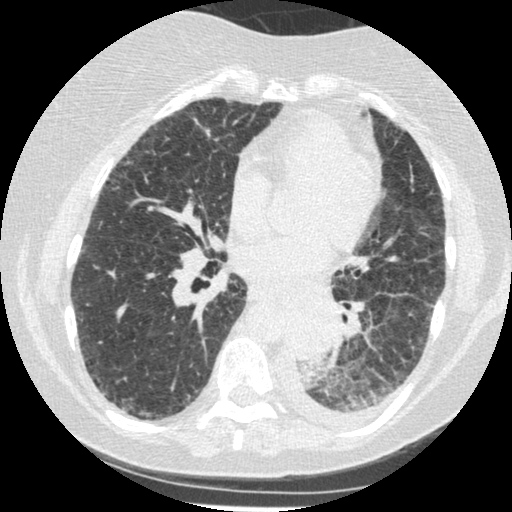
Low-dose screening chest CT, axial slice. Third screening round (two years after baseline). Lung window (W 1500 / L -600 HU). Slice 237 of 341 in the series. Female, age 60 years at enrolment. Former smoker at enrolment.
Expert reader's lesion annotation, bounding box <276,303,343,375> (left, top, right, bottom; pixels). The exam's reader record, not a measurement of the box and not confirmed to be the same lesion: non-calcified nodule or mass ≥4 mm, left lower lobe, 54 × 38 mm, smooth margins, soft tissue attenuation, pre-existing on the prior screen: yes; interval growth: yes. Official screen result: positive, other.